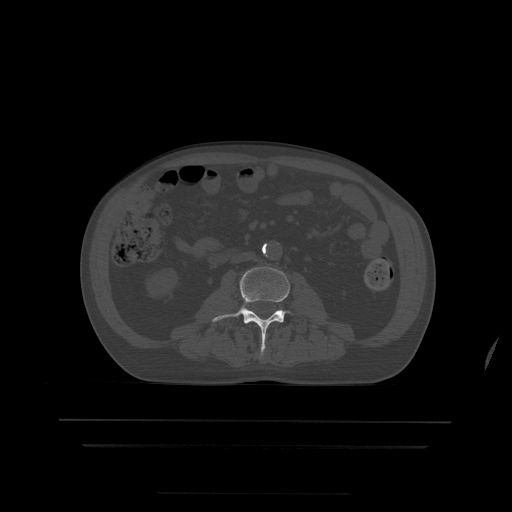
CT including the spine, one axial slice. Slice 119 of 522 in the series (ordered by position). Bone window (W 1800 / L 400 HU). 1.25 mm slice thickness. 512 × 512 image matrix, field of view 436 × 436 mm. Patient age 68 years. Case-level facts recorded for this patient, not image findings: primary cancer: urothelial.
Annotated regions visible in this slice (semi-automatic segmentation, software-assisted and operator-edited):
- L3 vertebra: bounding box <212,267,291,353> (left, top, right, bottom; pixels)